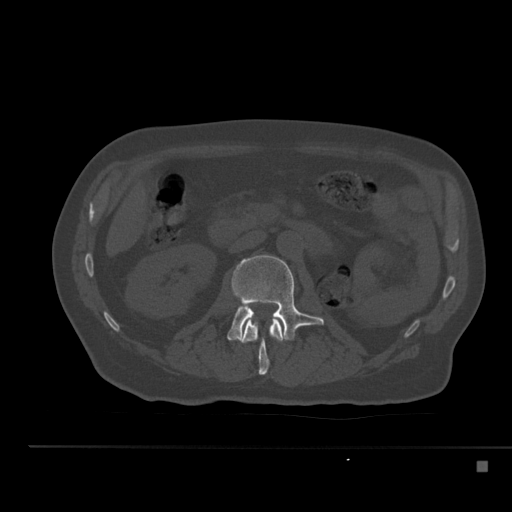
CT including the spine, one axial slice. Slice 193 of 517 in the series (ordered by position). 120 kVp. Bone window (W 1800 / L 400 HU). 1.5 mm slice thickness. 512 × 512 image matrix. Patient: male, 70 years. From the clinical record (not read from this slice): primary cancer: renal; vertebrae with lytic lesions (as recorded): T4, T6, T10, T12, L3, L4, L5.
Outlined on this slice (semi-automatic segmentation, software-assisted and operator-edited):
- L1 vertebra: bounding box (x1, y1, x2, y2) in pixels: (239, 317, 287, 375)
- L2 vertebra: (227, 255, 324, 340)